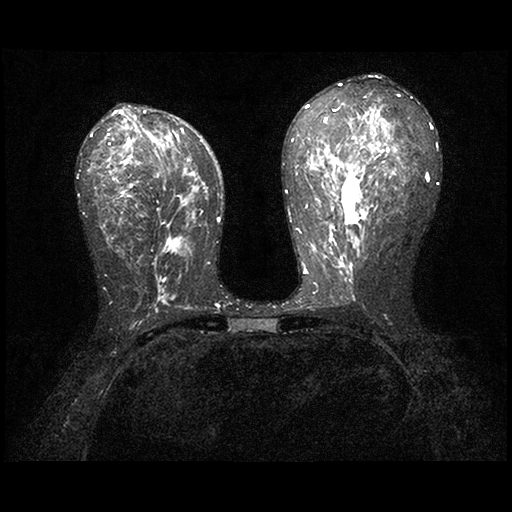
Breast MRI examination; 2 images, each one mid-volume slice chosen by position. Patient in her 50s.
Image 1: fluid-sensitive (T2/STIR) axial slice, series "STIR SENSE", slice 46 of 90.
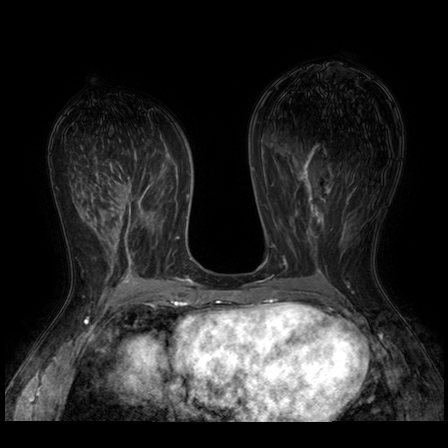
Image 2: axial dynamic contrast-enhanced T1-weighted image, series "AX BLISS_AUTO SENSE", slice 46 of 90, dynamic phase 5 of 8, 4 mm slice thickness.
MRI impression (as recorded): LEFT BREAST: There is moderate background enhancement. There is a large 8.0 x 6.5 x 5.5 cm seroma seen in the left upper central and upper inner breast within the surgical bed, without suspicious morphologic imaging features or suspicious kinetics on the dynamic series. There is expected peripheral hypervascularity seen in and around the surgical bed. No foci of suspicious enhancement, masses, or areas of architectural distortion seen within the left breast.There is a 1.4 x 0.9 x 1.3 cm (0.83 cc) left axillary kidney shaped lymphnode seen (image 67 series 40), with mixed kinetics, preserved fatty hilum - suggestive for reactive lymphnode - and an expected finding after recent surgery. There is no skin thickening, or nipple inversion present. RIGHT BREAST: There is moderate background enhancement. There are several surgical clips seen in the right upper central and upper outer breast, with expected post surgical mild architectural distortion and scar tissue. No foci of suspicious enhancement, masses, or areas of architectural distortion seen within the right breast. There is mild skin thickening - post radiation. No nipple inversion, or right axillary lymphadenopathy present. IMPRESSION:
1) No MRI evidence for residual malignancy in either breast.
2) Expected 8 cm left breast post surgical seroma.
3) Expected right breast post treatment changes.
4) Reactive left axillary lymphnode - post surgical; BI-RADS 2.
Patient-level pathology facts (from the clinical record, not from the images): receptor status (as recorded): ER pos (strong), PR pos (strong), HER2 pos; Ki-67 (as recorded): intermed prolif; pathology report notes: history of bilateral breast cancer, status post left
lumpectomy; clinical background (as recorded): age: 50s with history of right breast DCIS and new left breast cancer, status post recent breast conserving therapy with left lumpectomy, and status post right lumpectomy and radiation therapy last year.